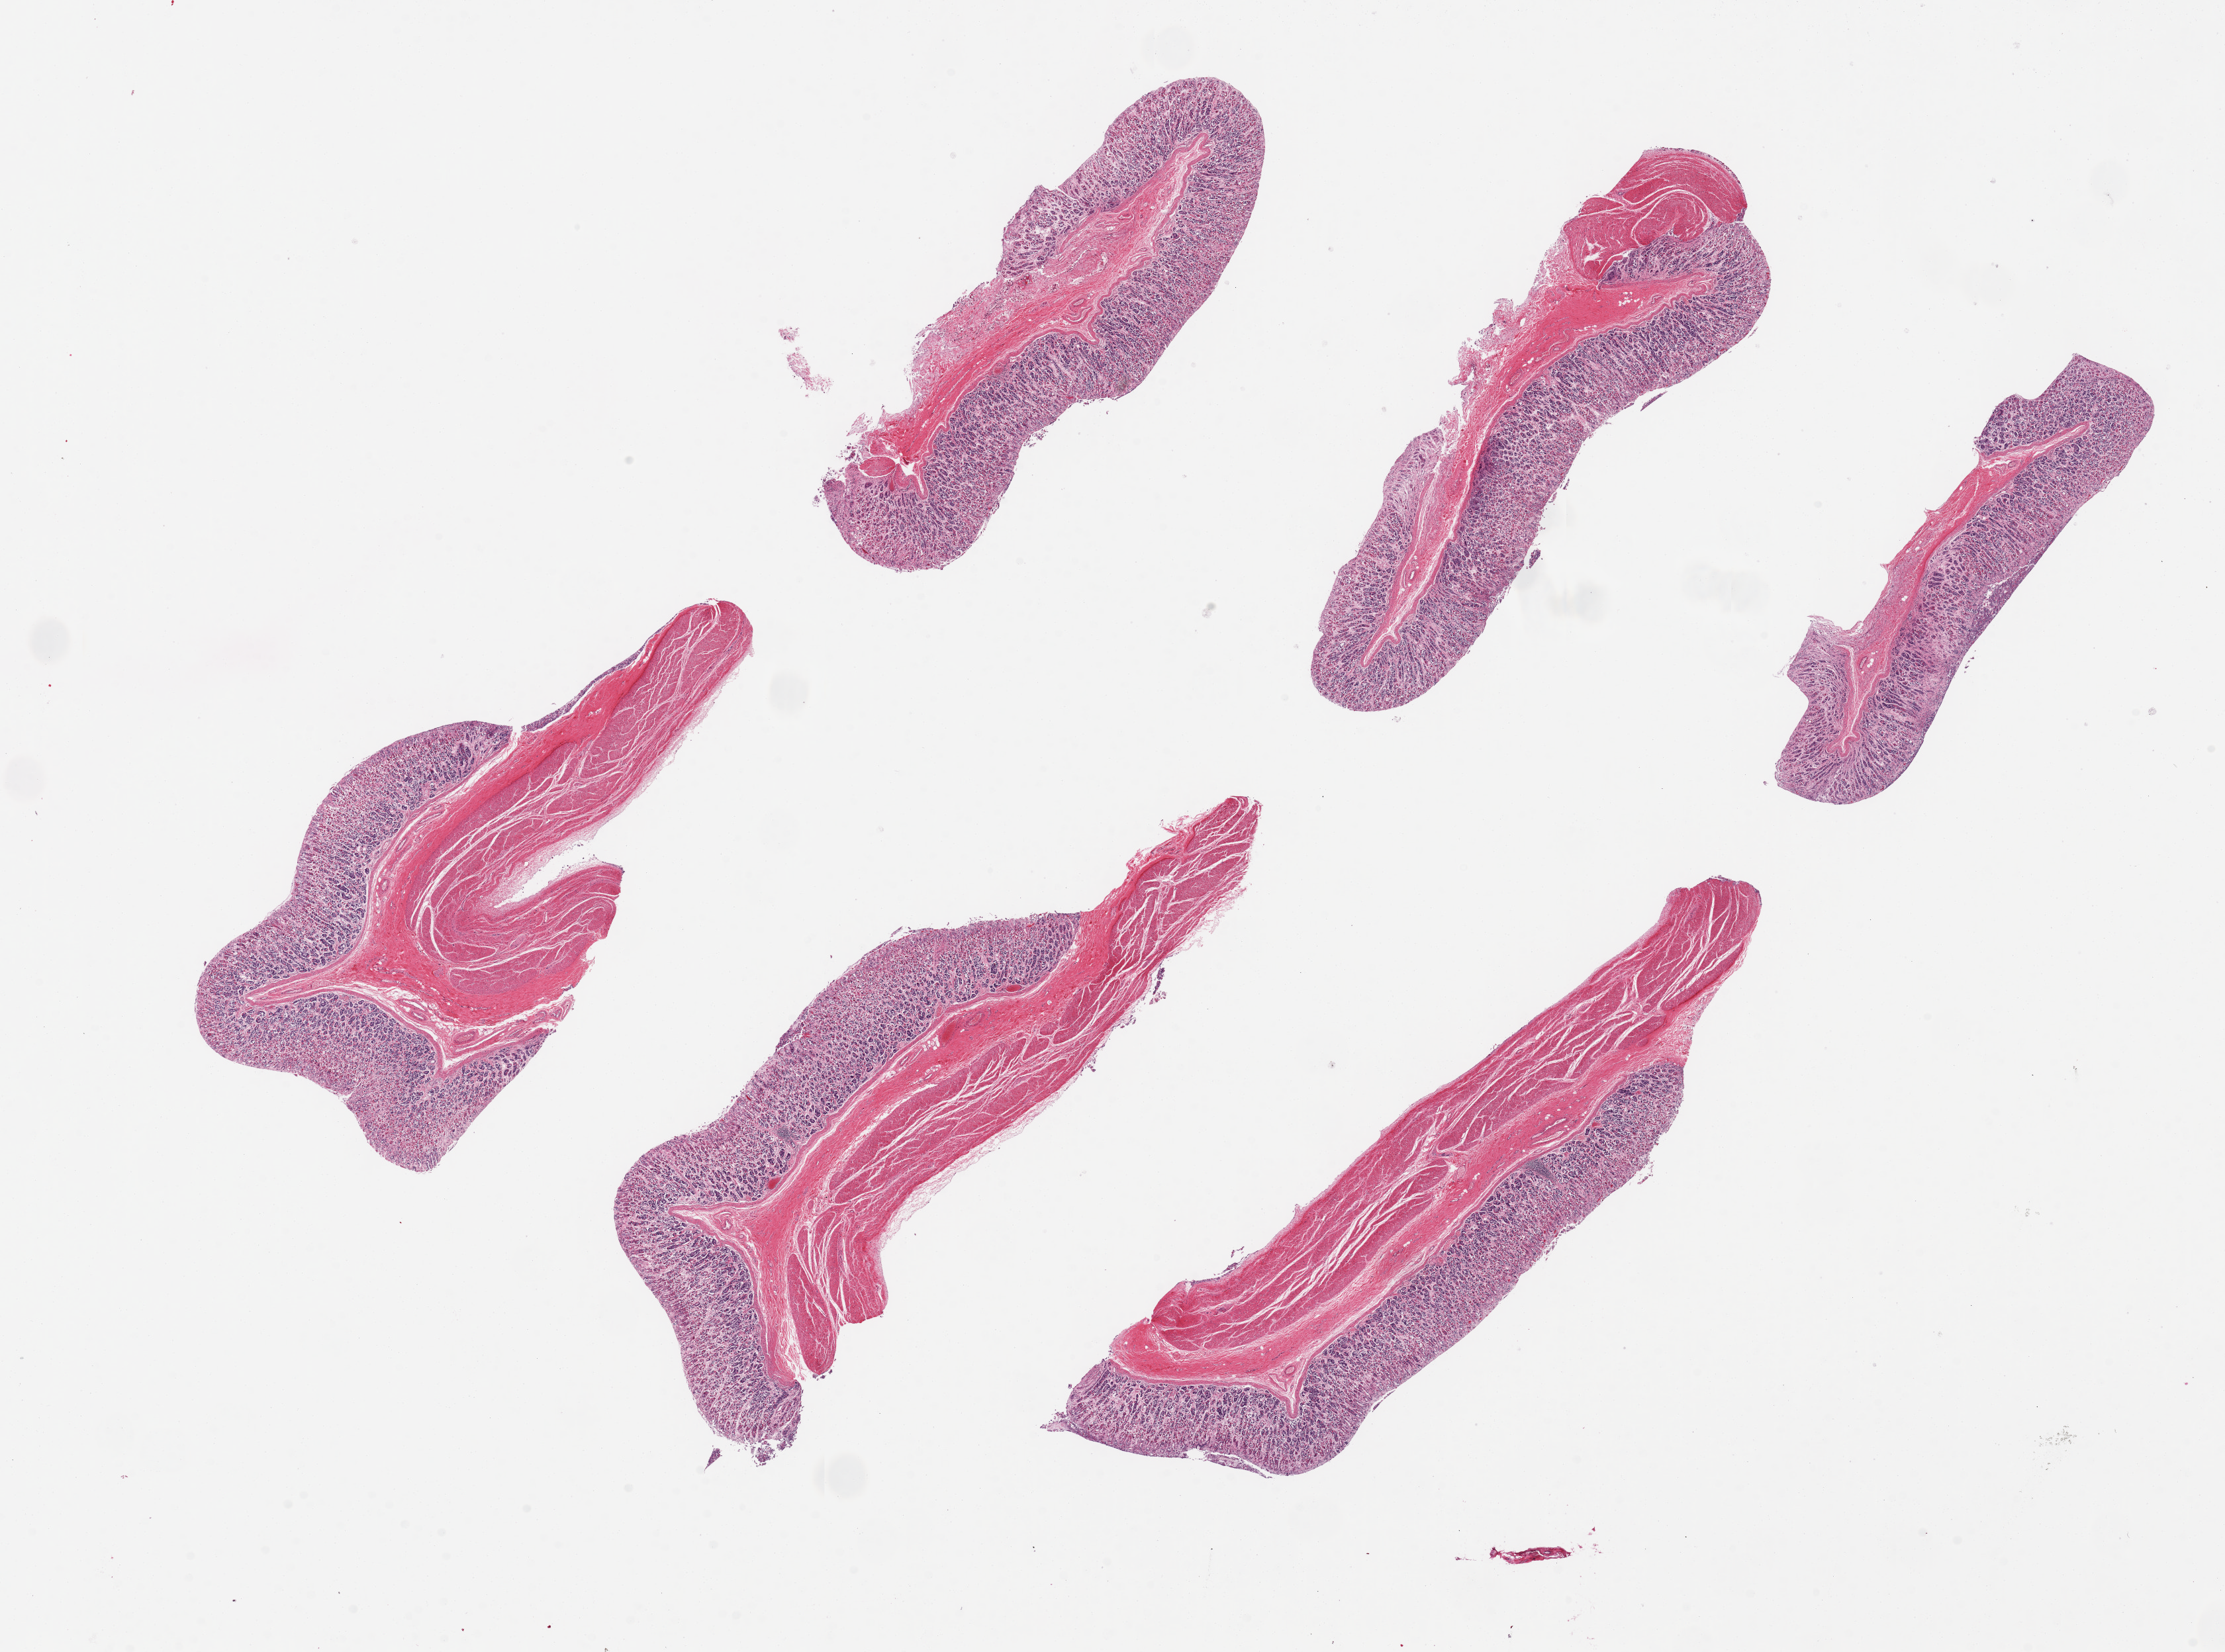
Digitized hematoxylin and eosin (H&E)-stained section, low-resolution overview of the scanned area, about 26.6 x 19.7 mm; PAXgene-fixed paraffin-embedded (PFPE) section; target tissue: stomach; donor tissue sample. Male donor.
- pathologist's review note for this sample: 6 pieces up to 10x2.5 mm